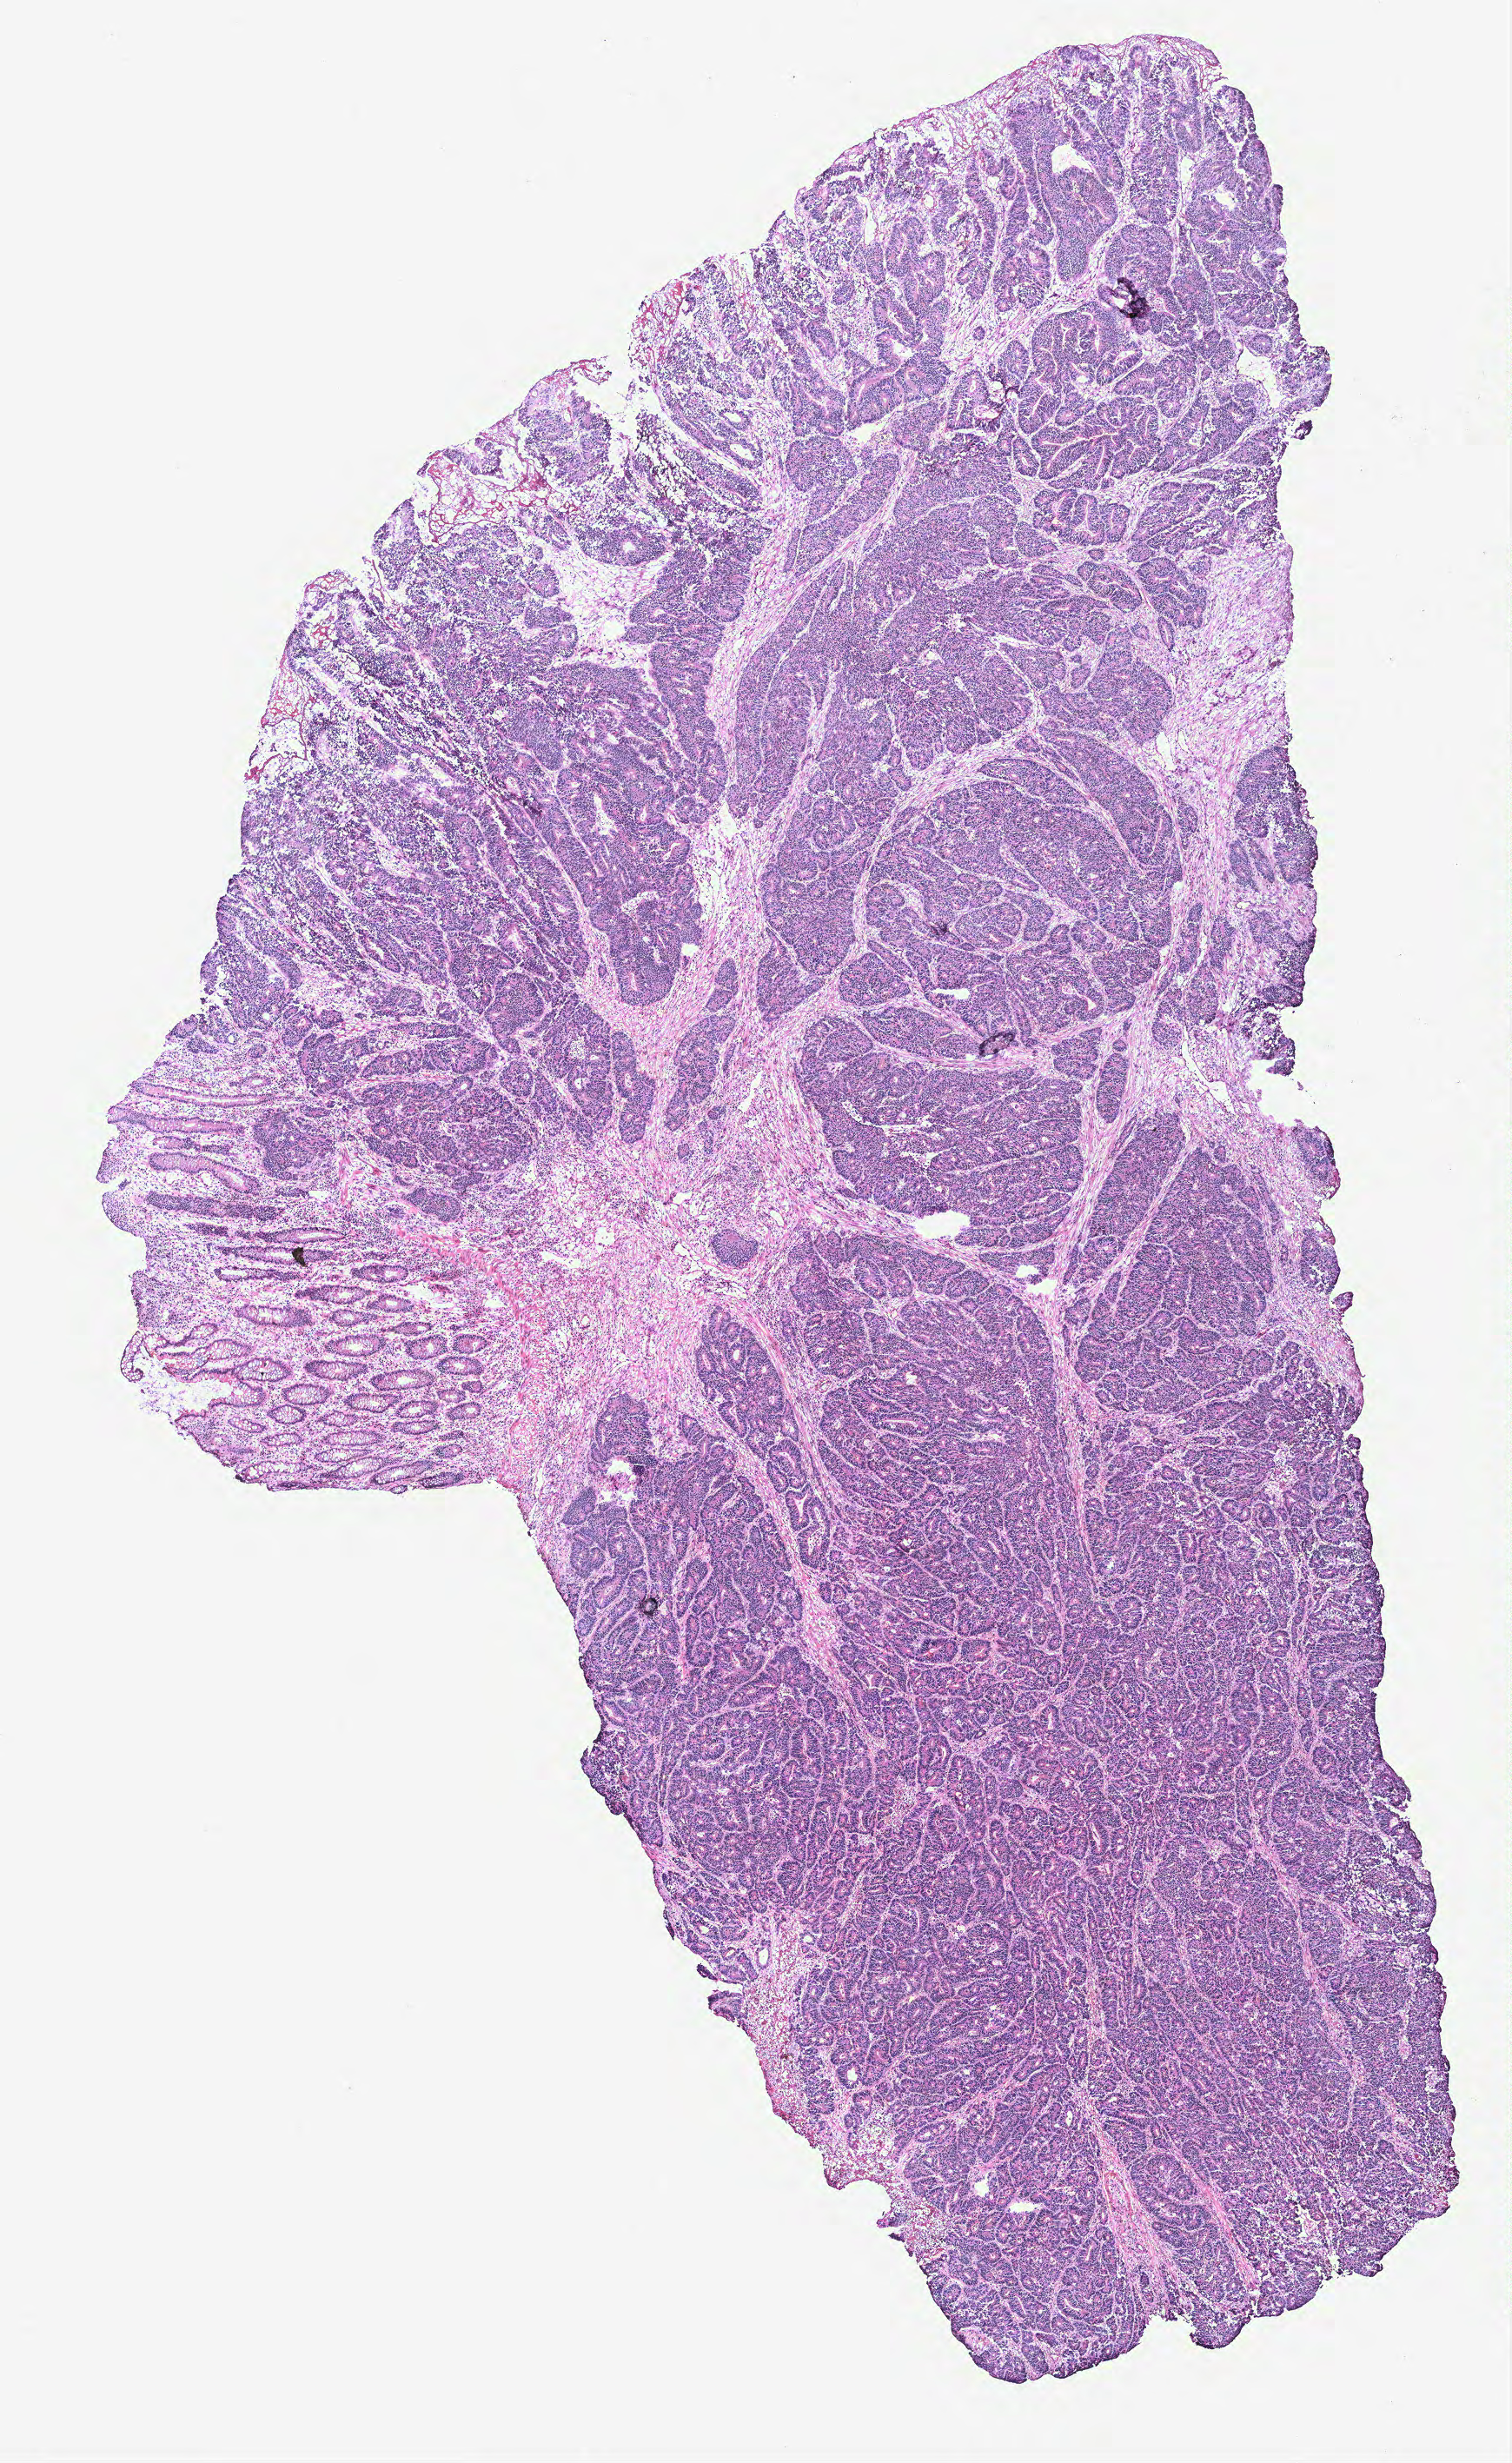
Digitized H&E-stained tissue section (whole slide), low-resolution overview of the scanned area, about 7.0 x 11.3 mm (slide scanned at 40x), normal (non-tumour) tissue sample, colon. Female, 66 y/o.
• this section: normal (non-tumour) tissue from the same patient
• patient diagnosis: Adenocarcinoma, NOS